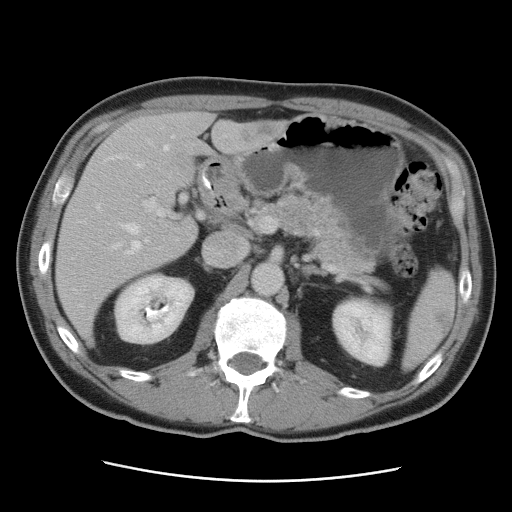
Contrast-enhanced abdominal CT, one axial slice; position 50 of 89 along the scan axis; 120 kVp; intravenous contrast given; soft-tissue window (W 400 / L 40 HU); 512 × 512 image matrix. Male patient, age 59 years. From the clinical record (not read from this slice): diagnosis: colorectal cancer liver metastases, imaged before liver resection; multiple liver metastases: yes; largest metastasis: 0.6 cm.
Outlined on this slice (expert manual segmentation):
- hepatic veins: bounding box (x1, y1, x2, y2) in pixels: (96, 135, 226, 255)
- liver: (55, 113, 289, 343)
- planned liver remnant (the part of the liver to remain after resection): (71, 113, 214, 243)
- portal vein (with intrahepatic branches): (143, 198, 262, 242)
- liver metastasis: (242, 123, 281, 142)